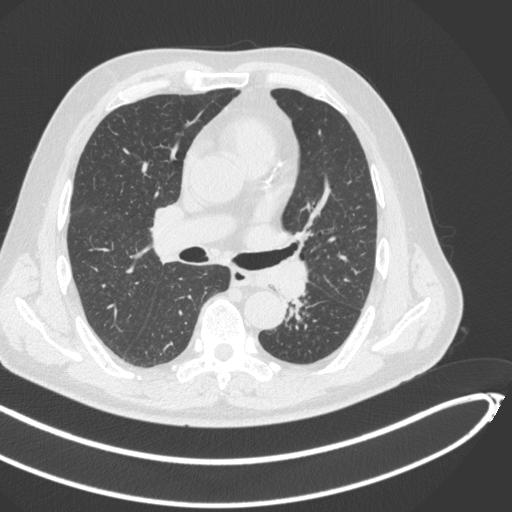
Chest CT, one axial slice; slice 266 of 466 in the series (ordered by position); lung window (W 1500 / L -600 HU); 1 mm slice thickness; 512 × 512 image matrix, field of view 400 × 400 mm. Male patient, age 64 years. Case-level facts recorded for this patient, not image findings: clinical TNM (as recorded): T1c N0 M0; histopathological grade: G2.
Annotated regions visible in this slice (rectangle marked by the reading radiologist):
- lung tumour (recorded histology: squamous cell carcinoma): bounding box [x1, y1, x2, y2] px = [256, 253, 311, 303]